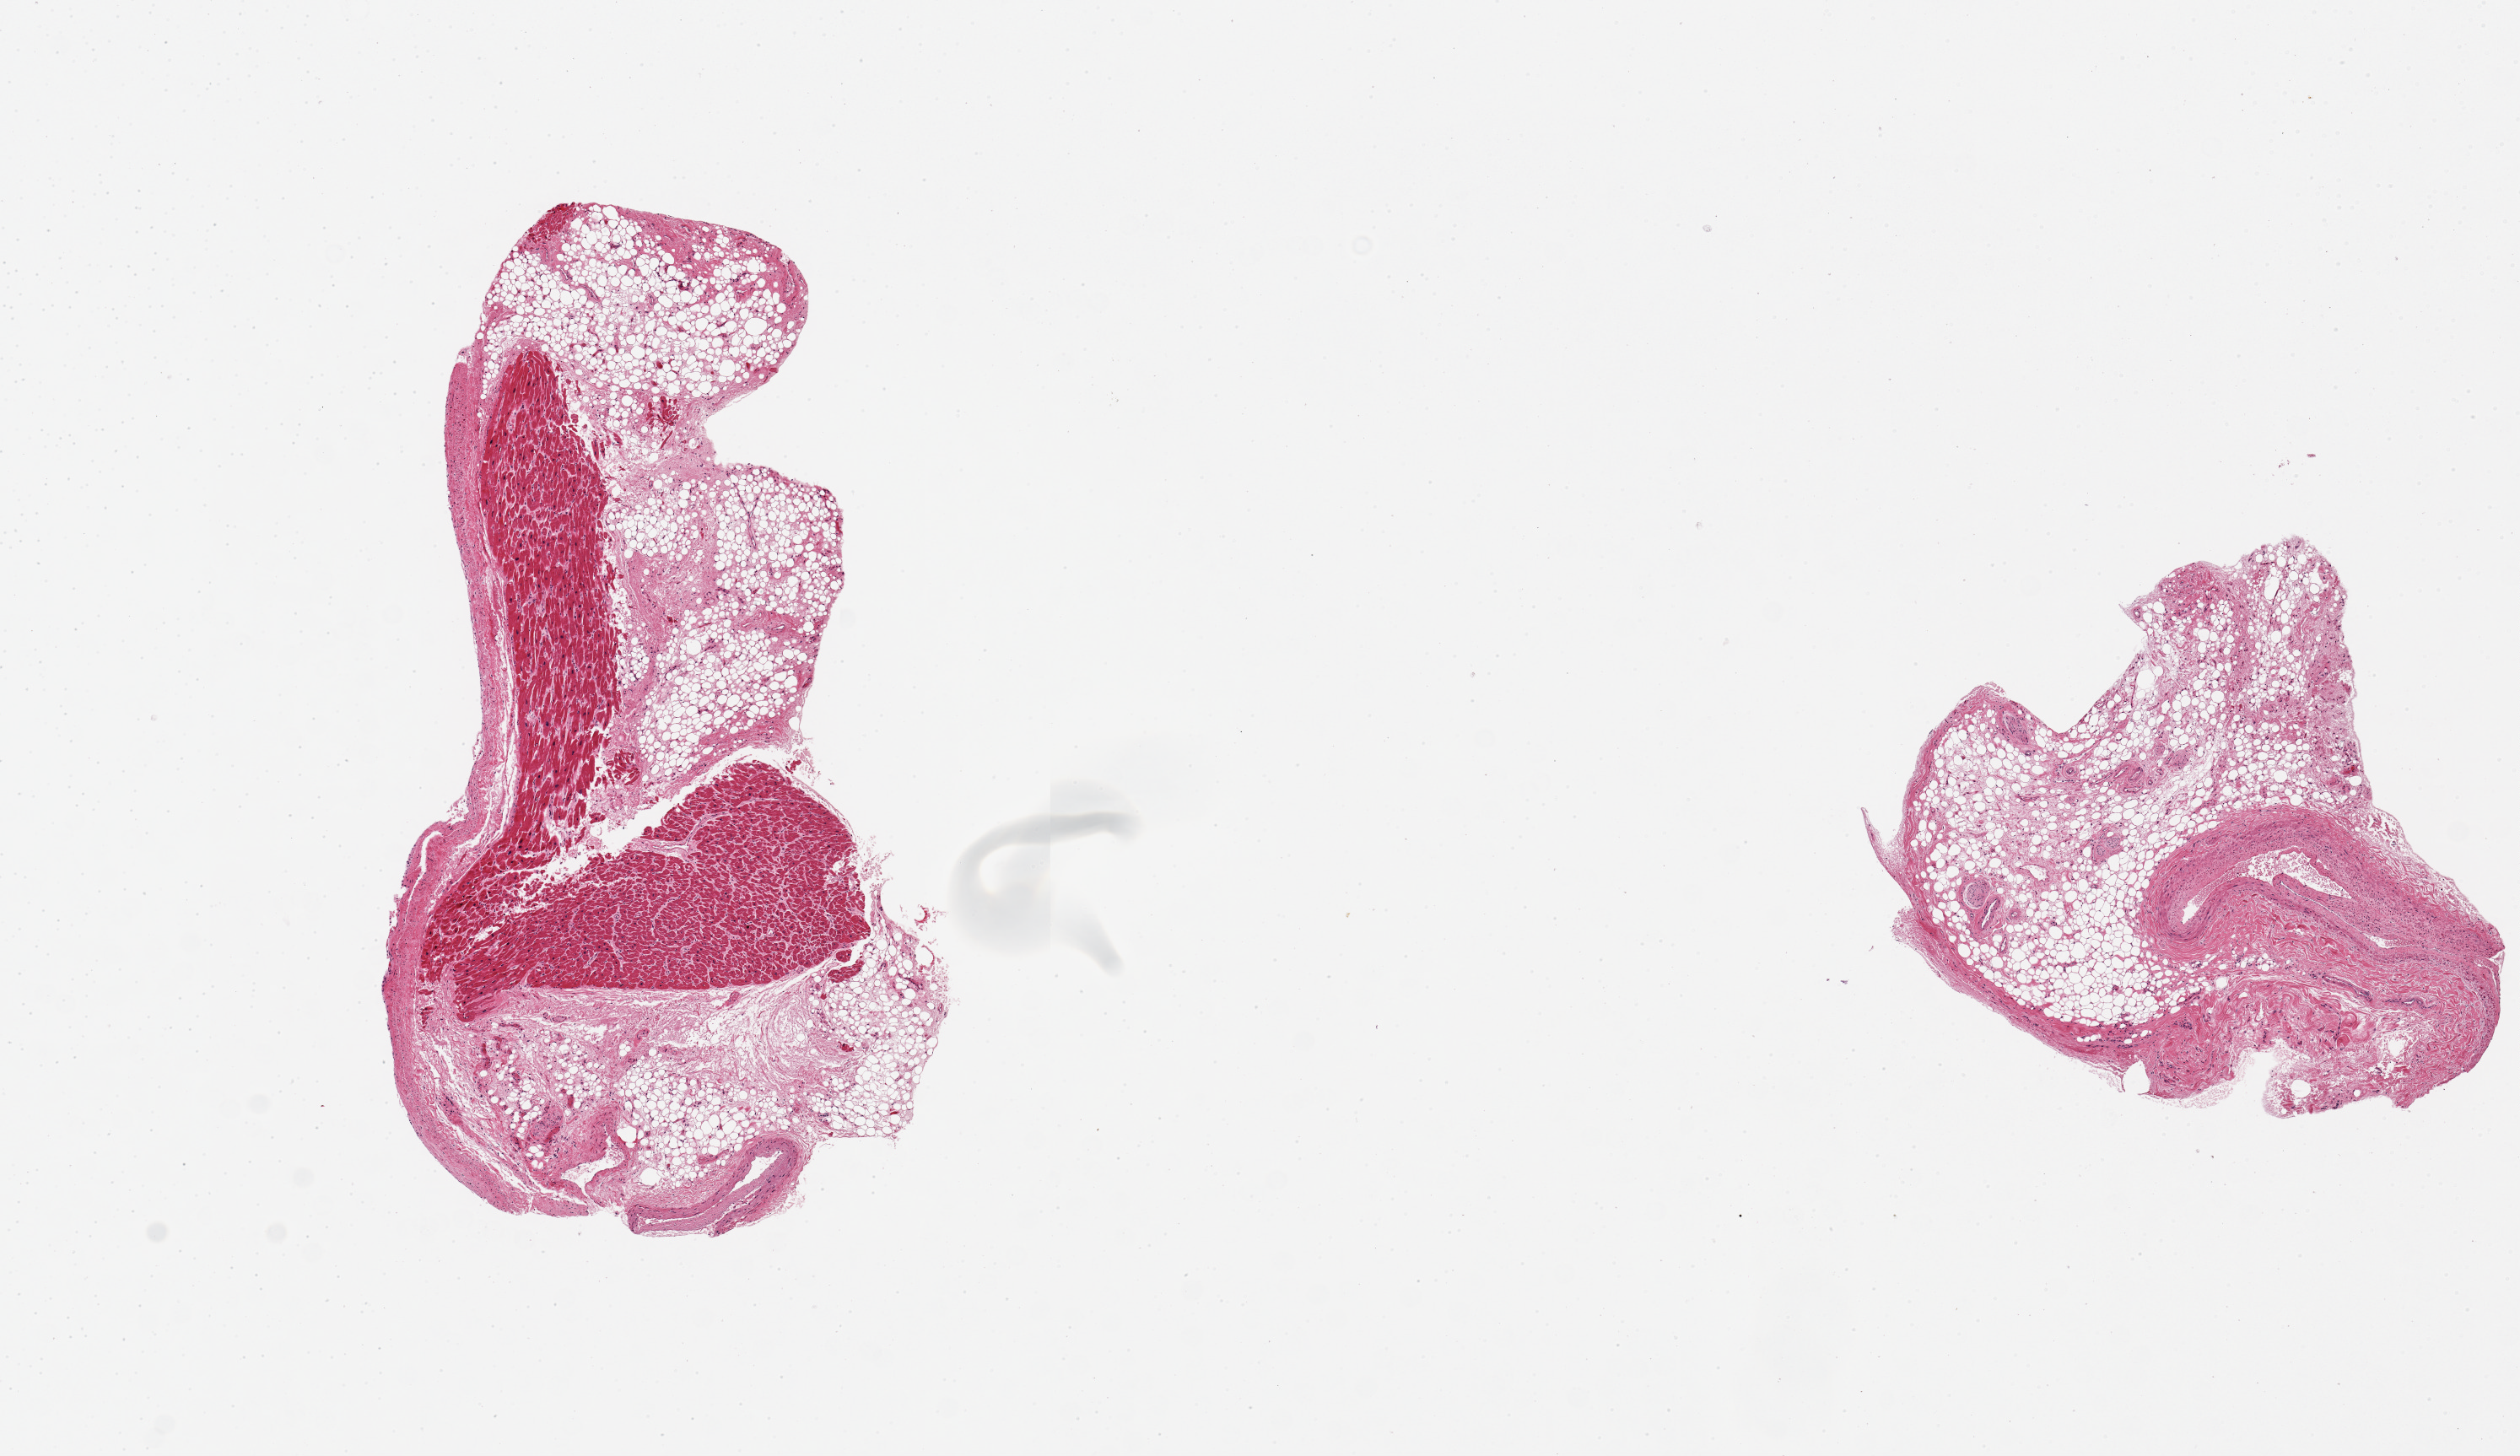
Hematoxylin and eosin (H&E) whole-slide image — shown as a low-resolution overview of the whole scanned area (about 11.8 x 6.8 mm, acquisition: 20x scan), PAXgene-fixed, paraffin-embedded tissue, sampled site (target tissue): coronary artery, tissue donor sample.
Review note (as recorded): 2 pieces; one piece is 80% fibrofatty, limited value; other is >95% muscle and fat, no value as artery specimen.